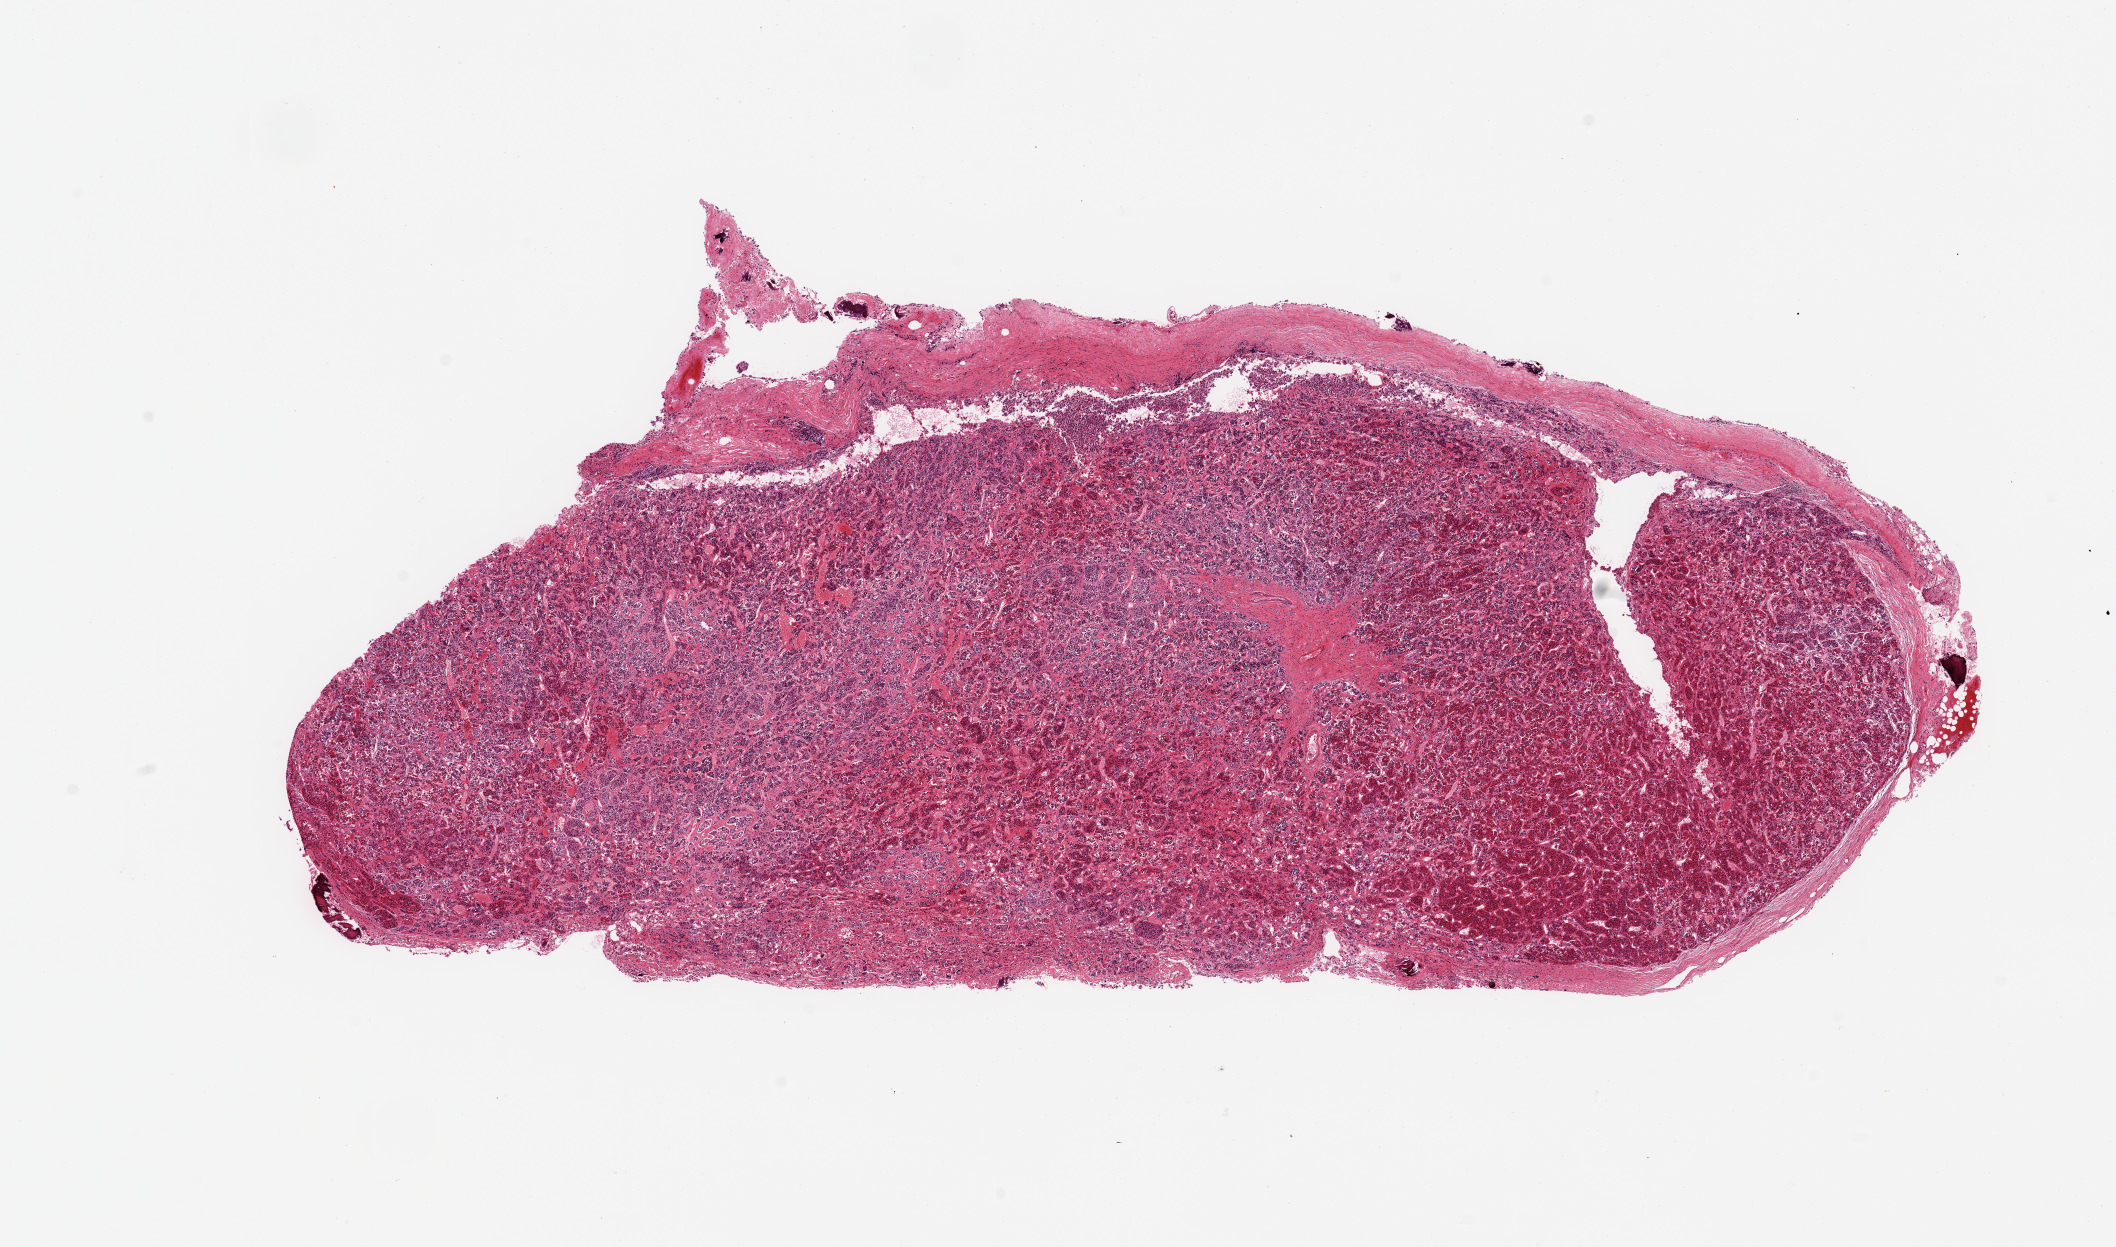
Digitized hematoxylin and eosin (H&E)-stained section, shown as a low-resolution overview of the whole scanned area (about 16.7 x 9.9 mm). PAXgene-fixed, paraffin-embedded tissue. Section of pituitary (target tissue). Donor tissue sample. Female donor.
Review note (as recorded): 1 piece; adenohypophysis.